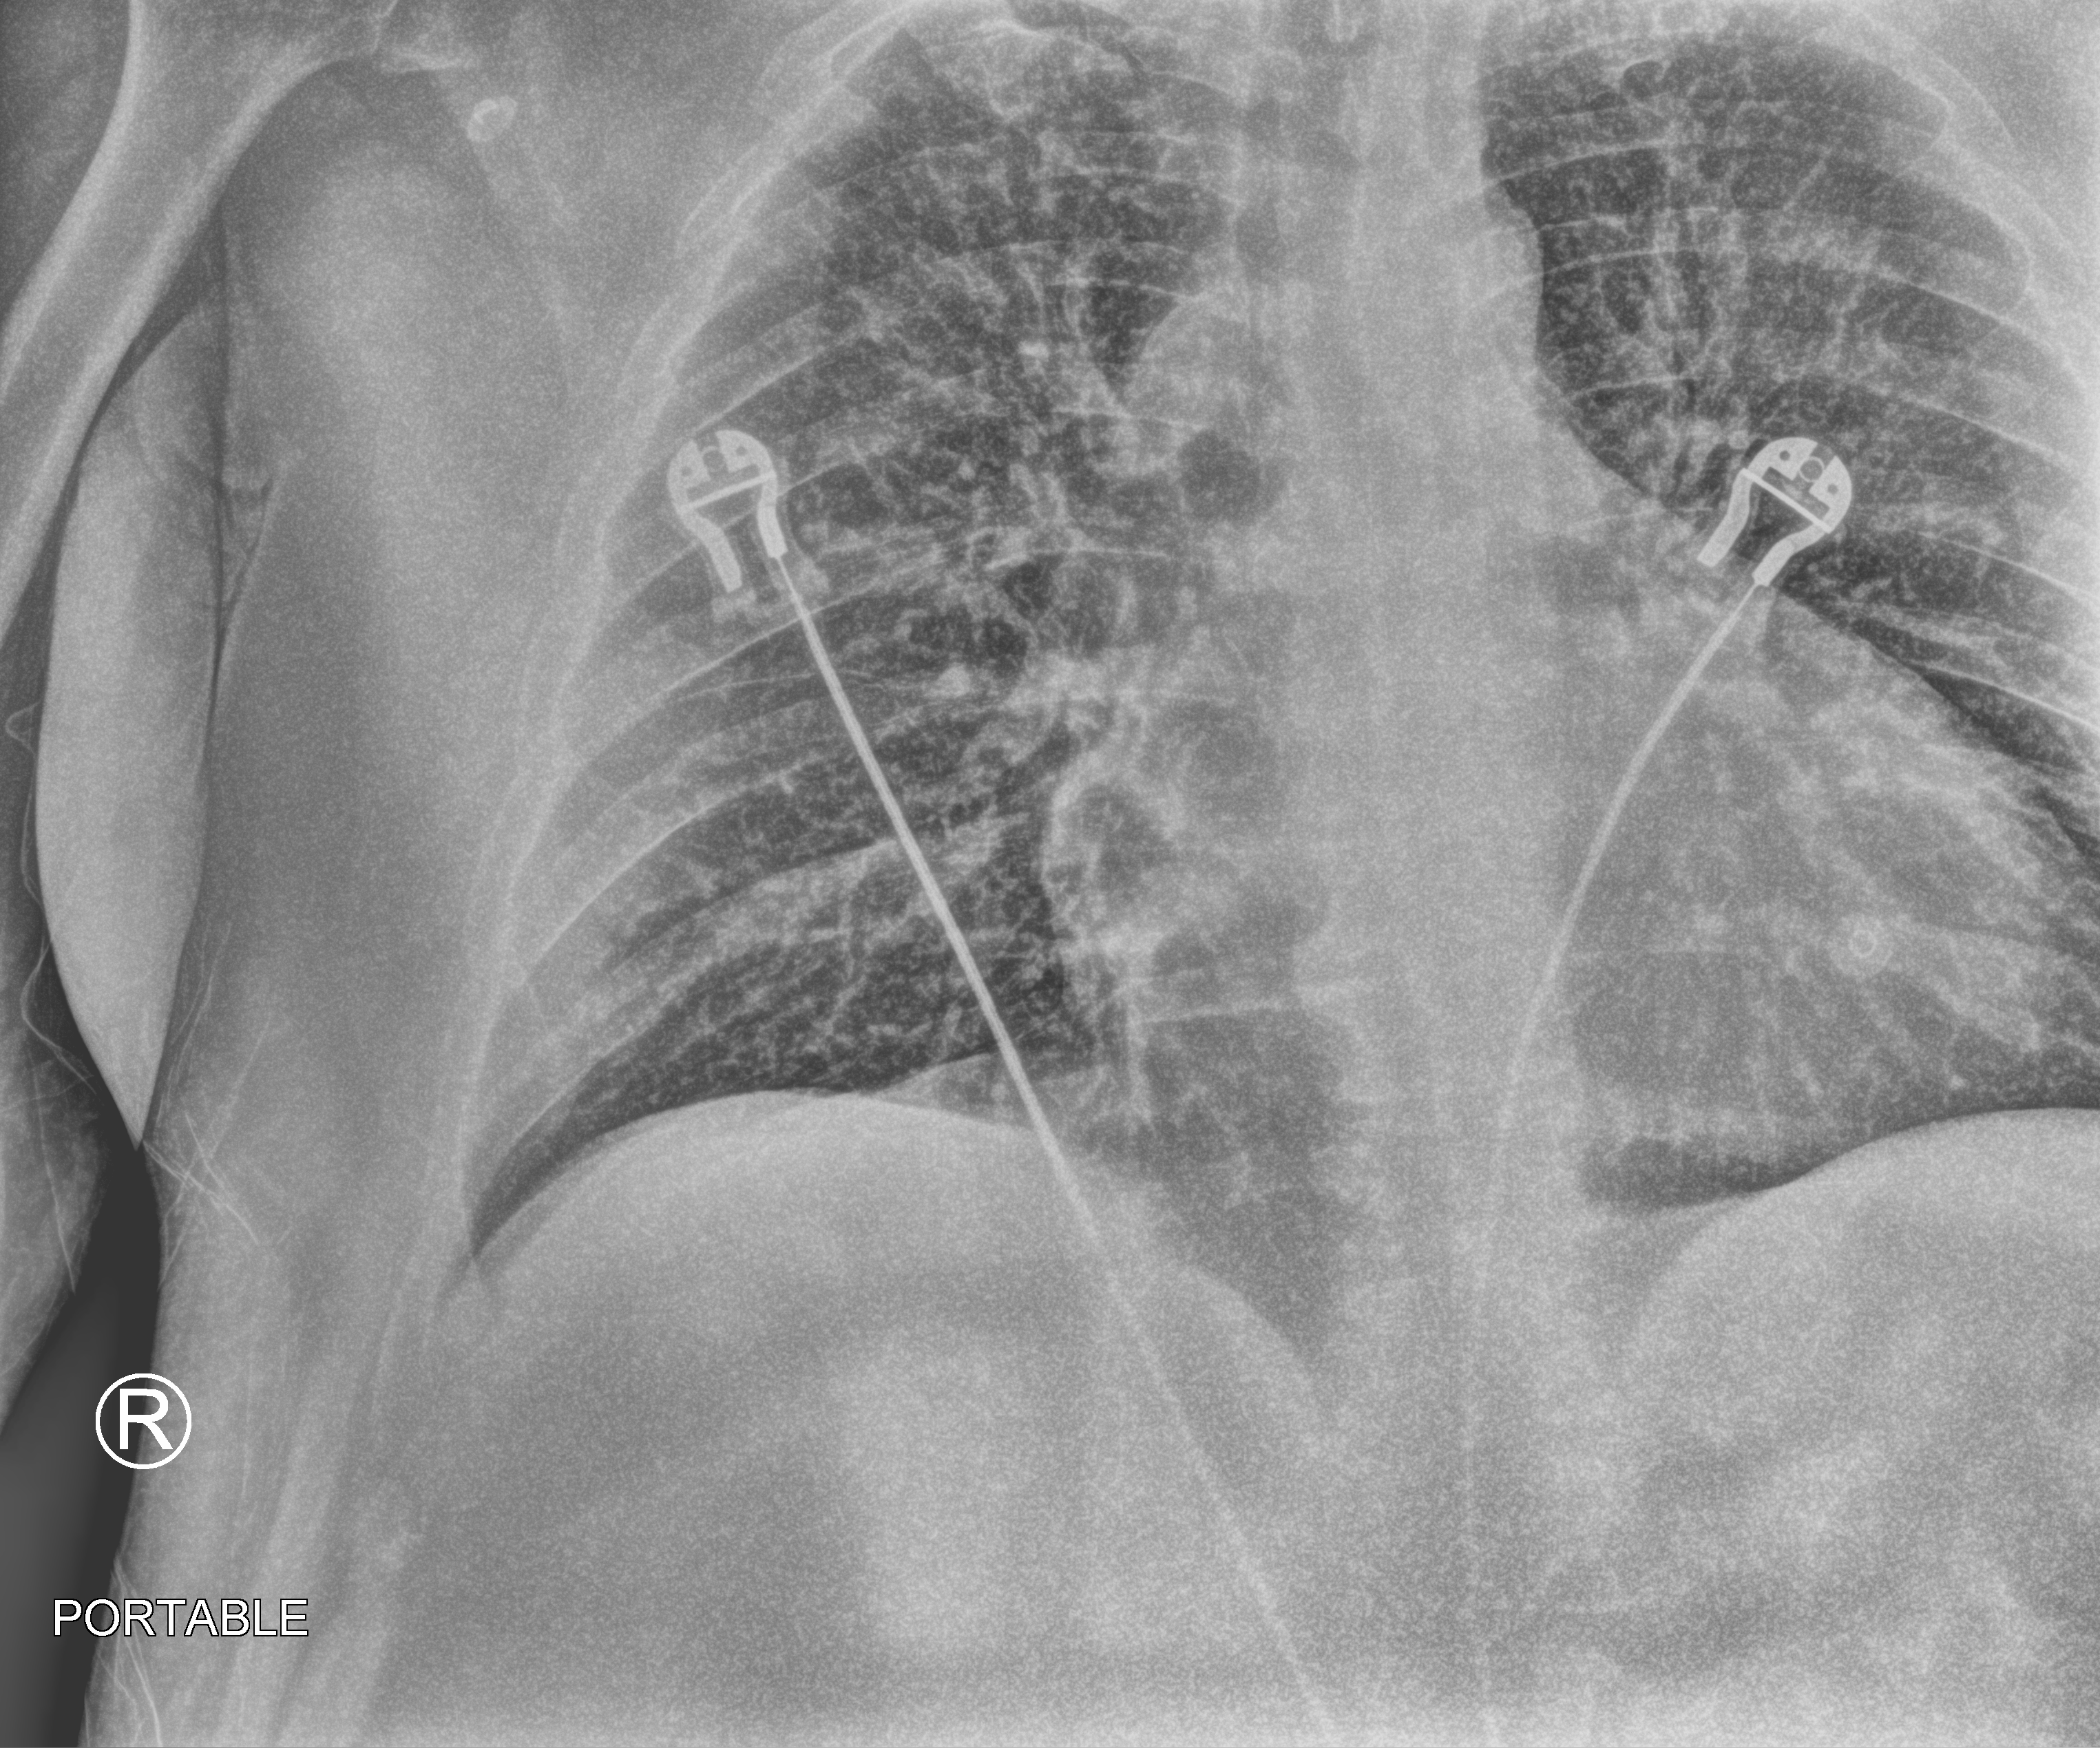
Bedside chest radiograph (computed radiography), anteroposterior (AP) projection. Male patient hospitalised with COVID-19, age 18–59 years.
From the hospital-stay record, not from the radiograph (when in the stay this image was taken is not recorded): mechanically ventilated during this hospital stay: no; hypertension (admission record): yes; other chronic lung disease (admission record): no.